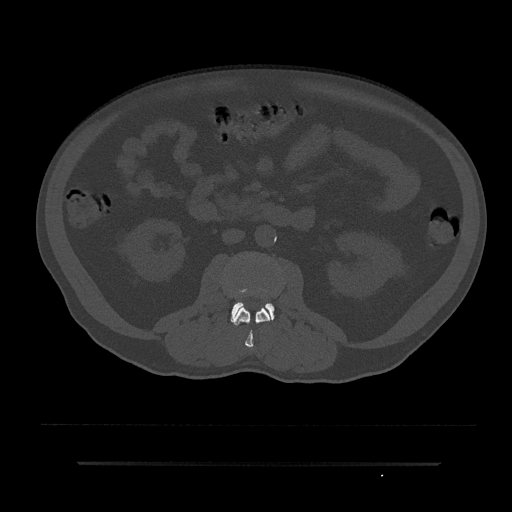
CT including the spine, one axial slice; slice 40 of 797 in the series (ordered by position); 120 kVp; bone window (W 1800 / L 400 HU); 0.5 mm slice thickness; 512 × 512 image matrix, field of view 464 × 464 mm. Male patient, age 59 years. Case-level facts recorded for this patient, not image findings: primary cancer: bile ducts; vertebrae with lytic lesions (as recorded): T10.
Structures marked on this image (semi-automatically segmented with operator editing):
- L2 vertebra: bounding box (x1, y1, x2, y2) in pixels: (233, 306, 272, 348)
- L3 vertebra: (231, 302, 274, 323)